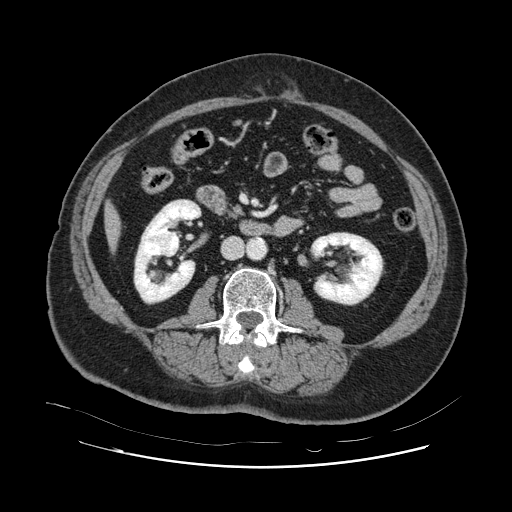
Contrast-enhanced abdominal CT, one axial slice. Position 20 of 132 along the scan axis. Intravenous contrast given. Soft-tissue window (W 400 / L 40 HU). 2.5 mm slice thickness. 512 × 512 image matrix, field of view 391 × 391 mm. Female patient, age 73 years. From the clinical record (not read from this slice): diagnosis: colorectal cancer liver metastases, imaged before liver resection; multiple liver metastases: no; largest metastasis: 7 cm; chemotherapy before resection: yes.
Annotated regions visible in this slice (outlined manually by an expert reader):
- liver: bounding box <107,208,119,242> (left, top, right, bottom; pixels)
- planned liver remnant (the part of the liver to remain after resection): <107,207,120,243>